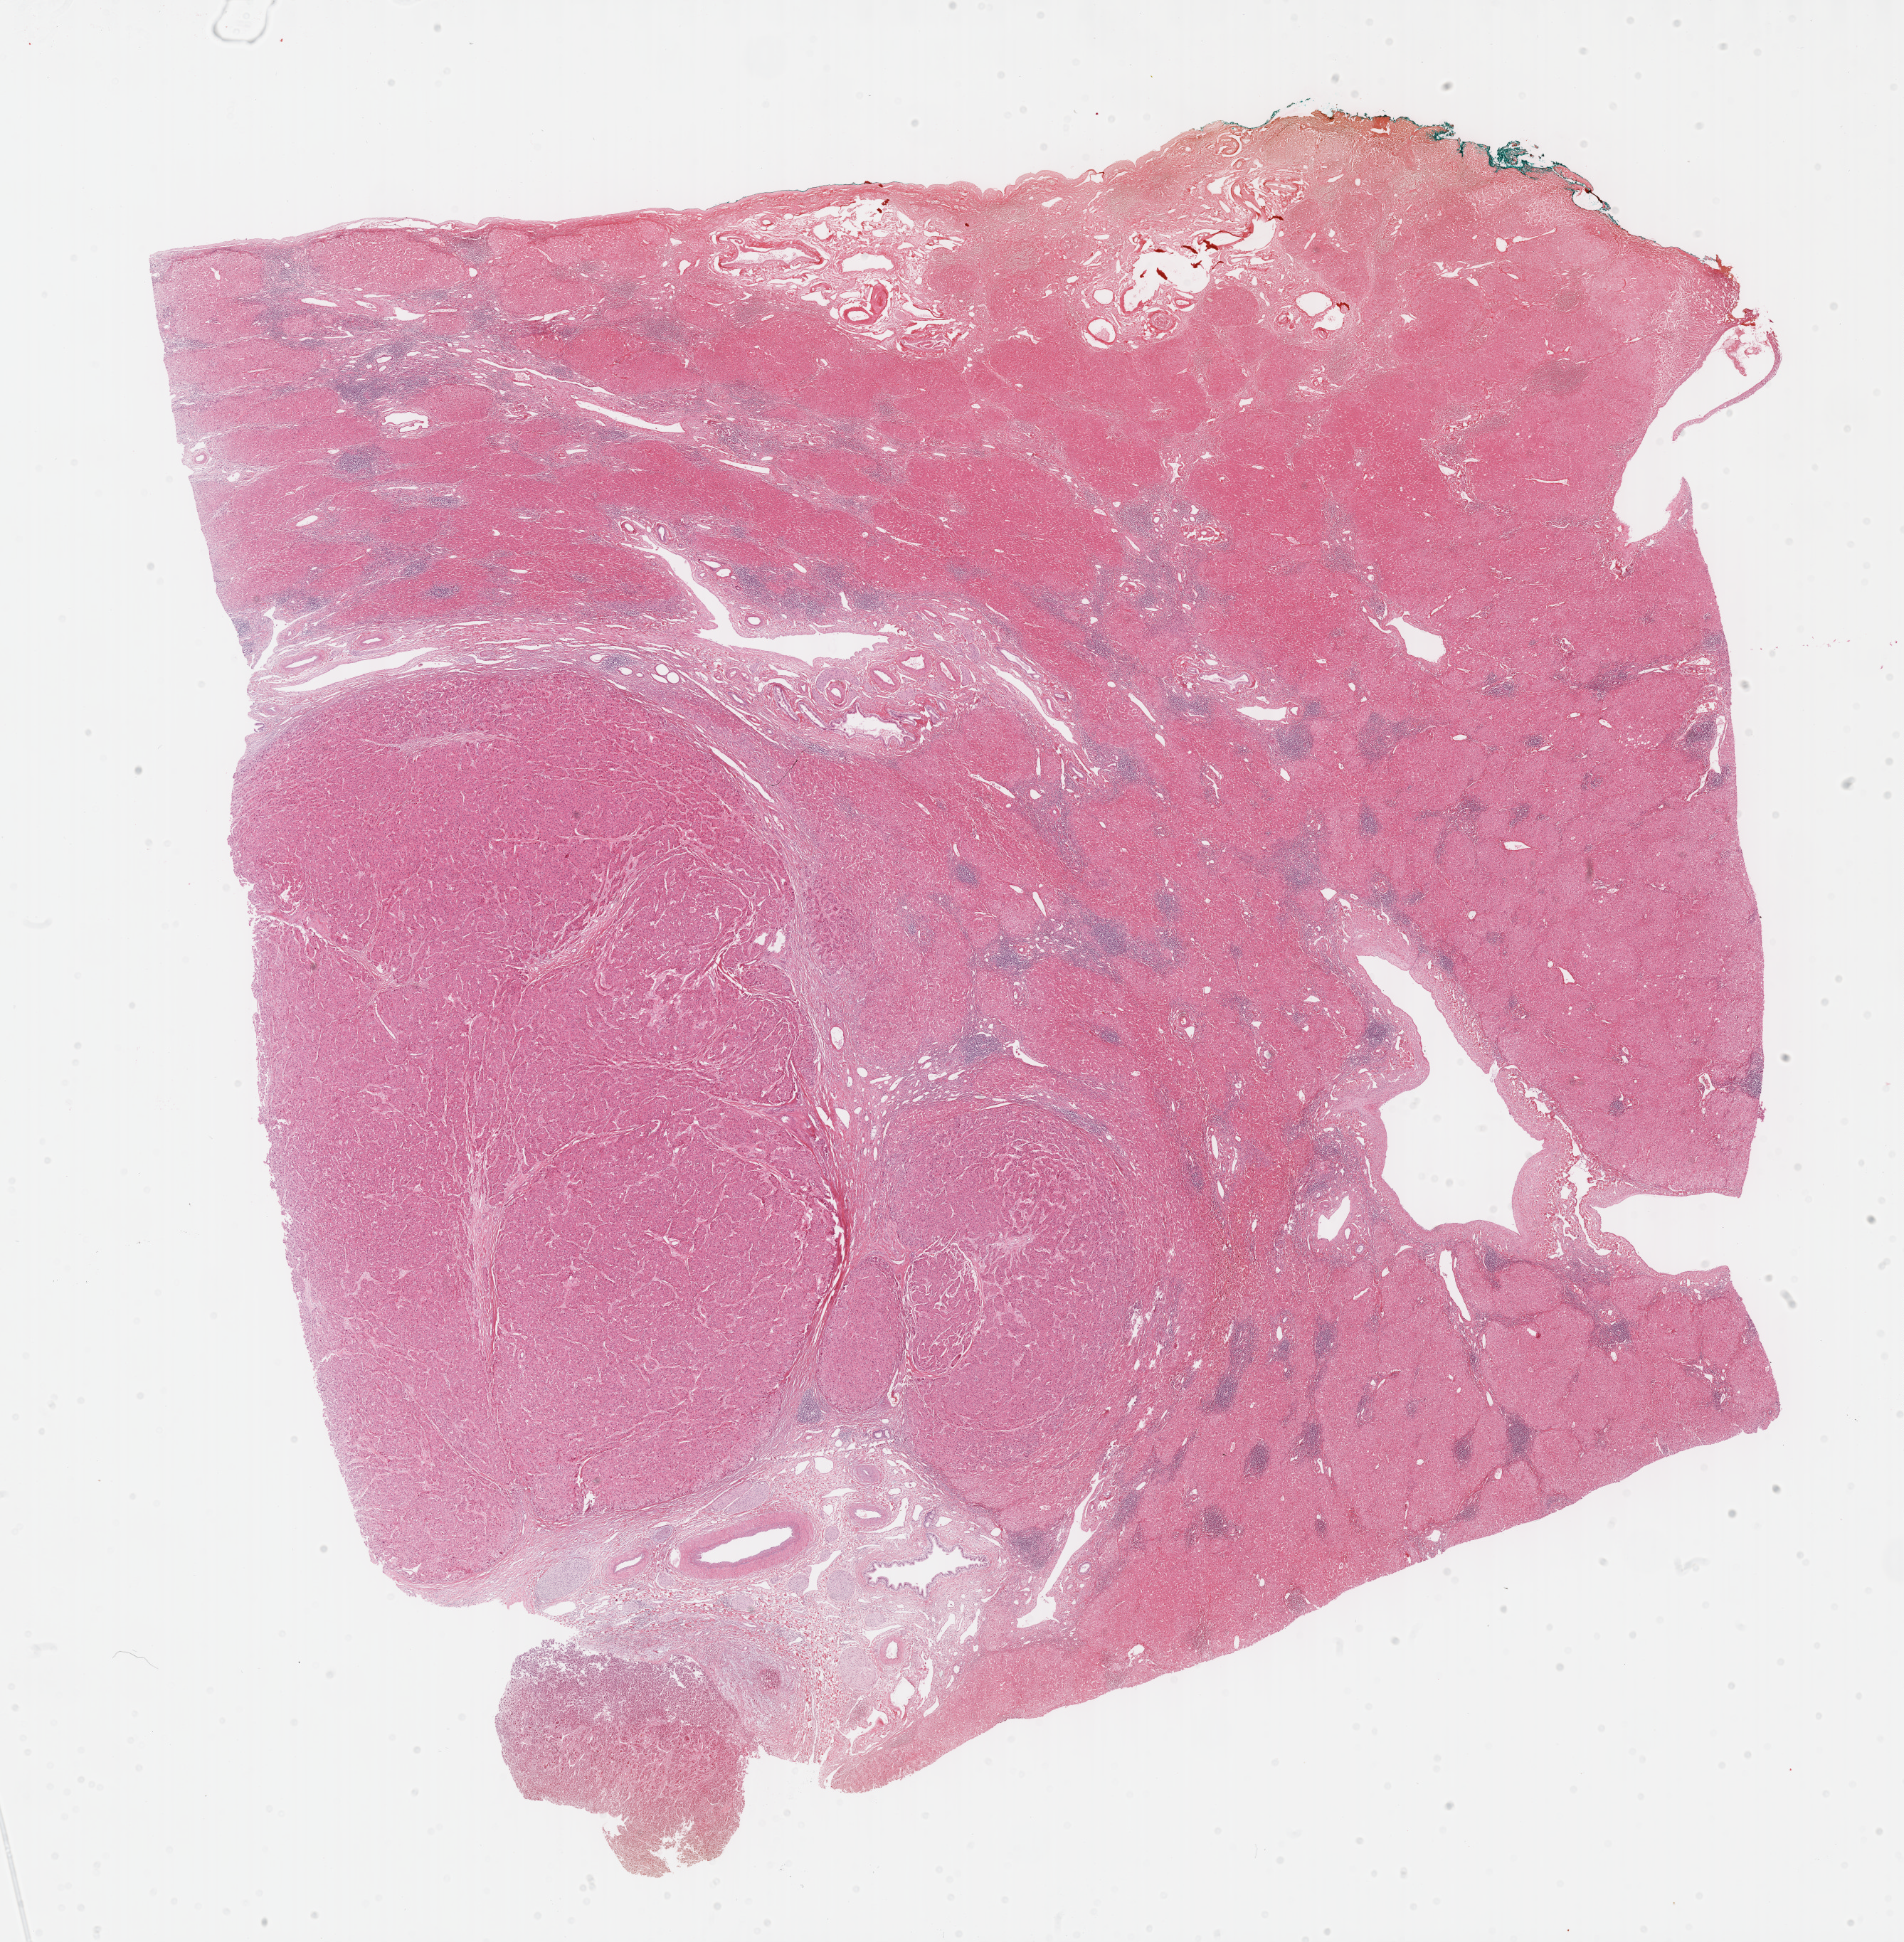
Digitized H&E-stained tissue section (whole slide) — shown as a low-resolution overview of the whole scanned area (about 21.6 x 22.1 mm, from a 40x scan); formalin-fixed paraffin-embedded (FFPE) diagnostic section; primary tumour sample from the liver. Male, age 59 years at initial diagnosis. Histologic grade: G3 (poorly differentiated).
Diagnosis: Hepatocellular carcinoma, NOS. AJCC pathologic stage: I.